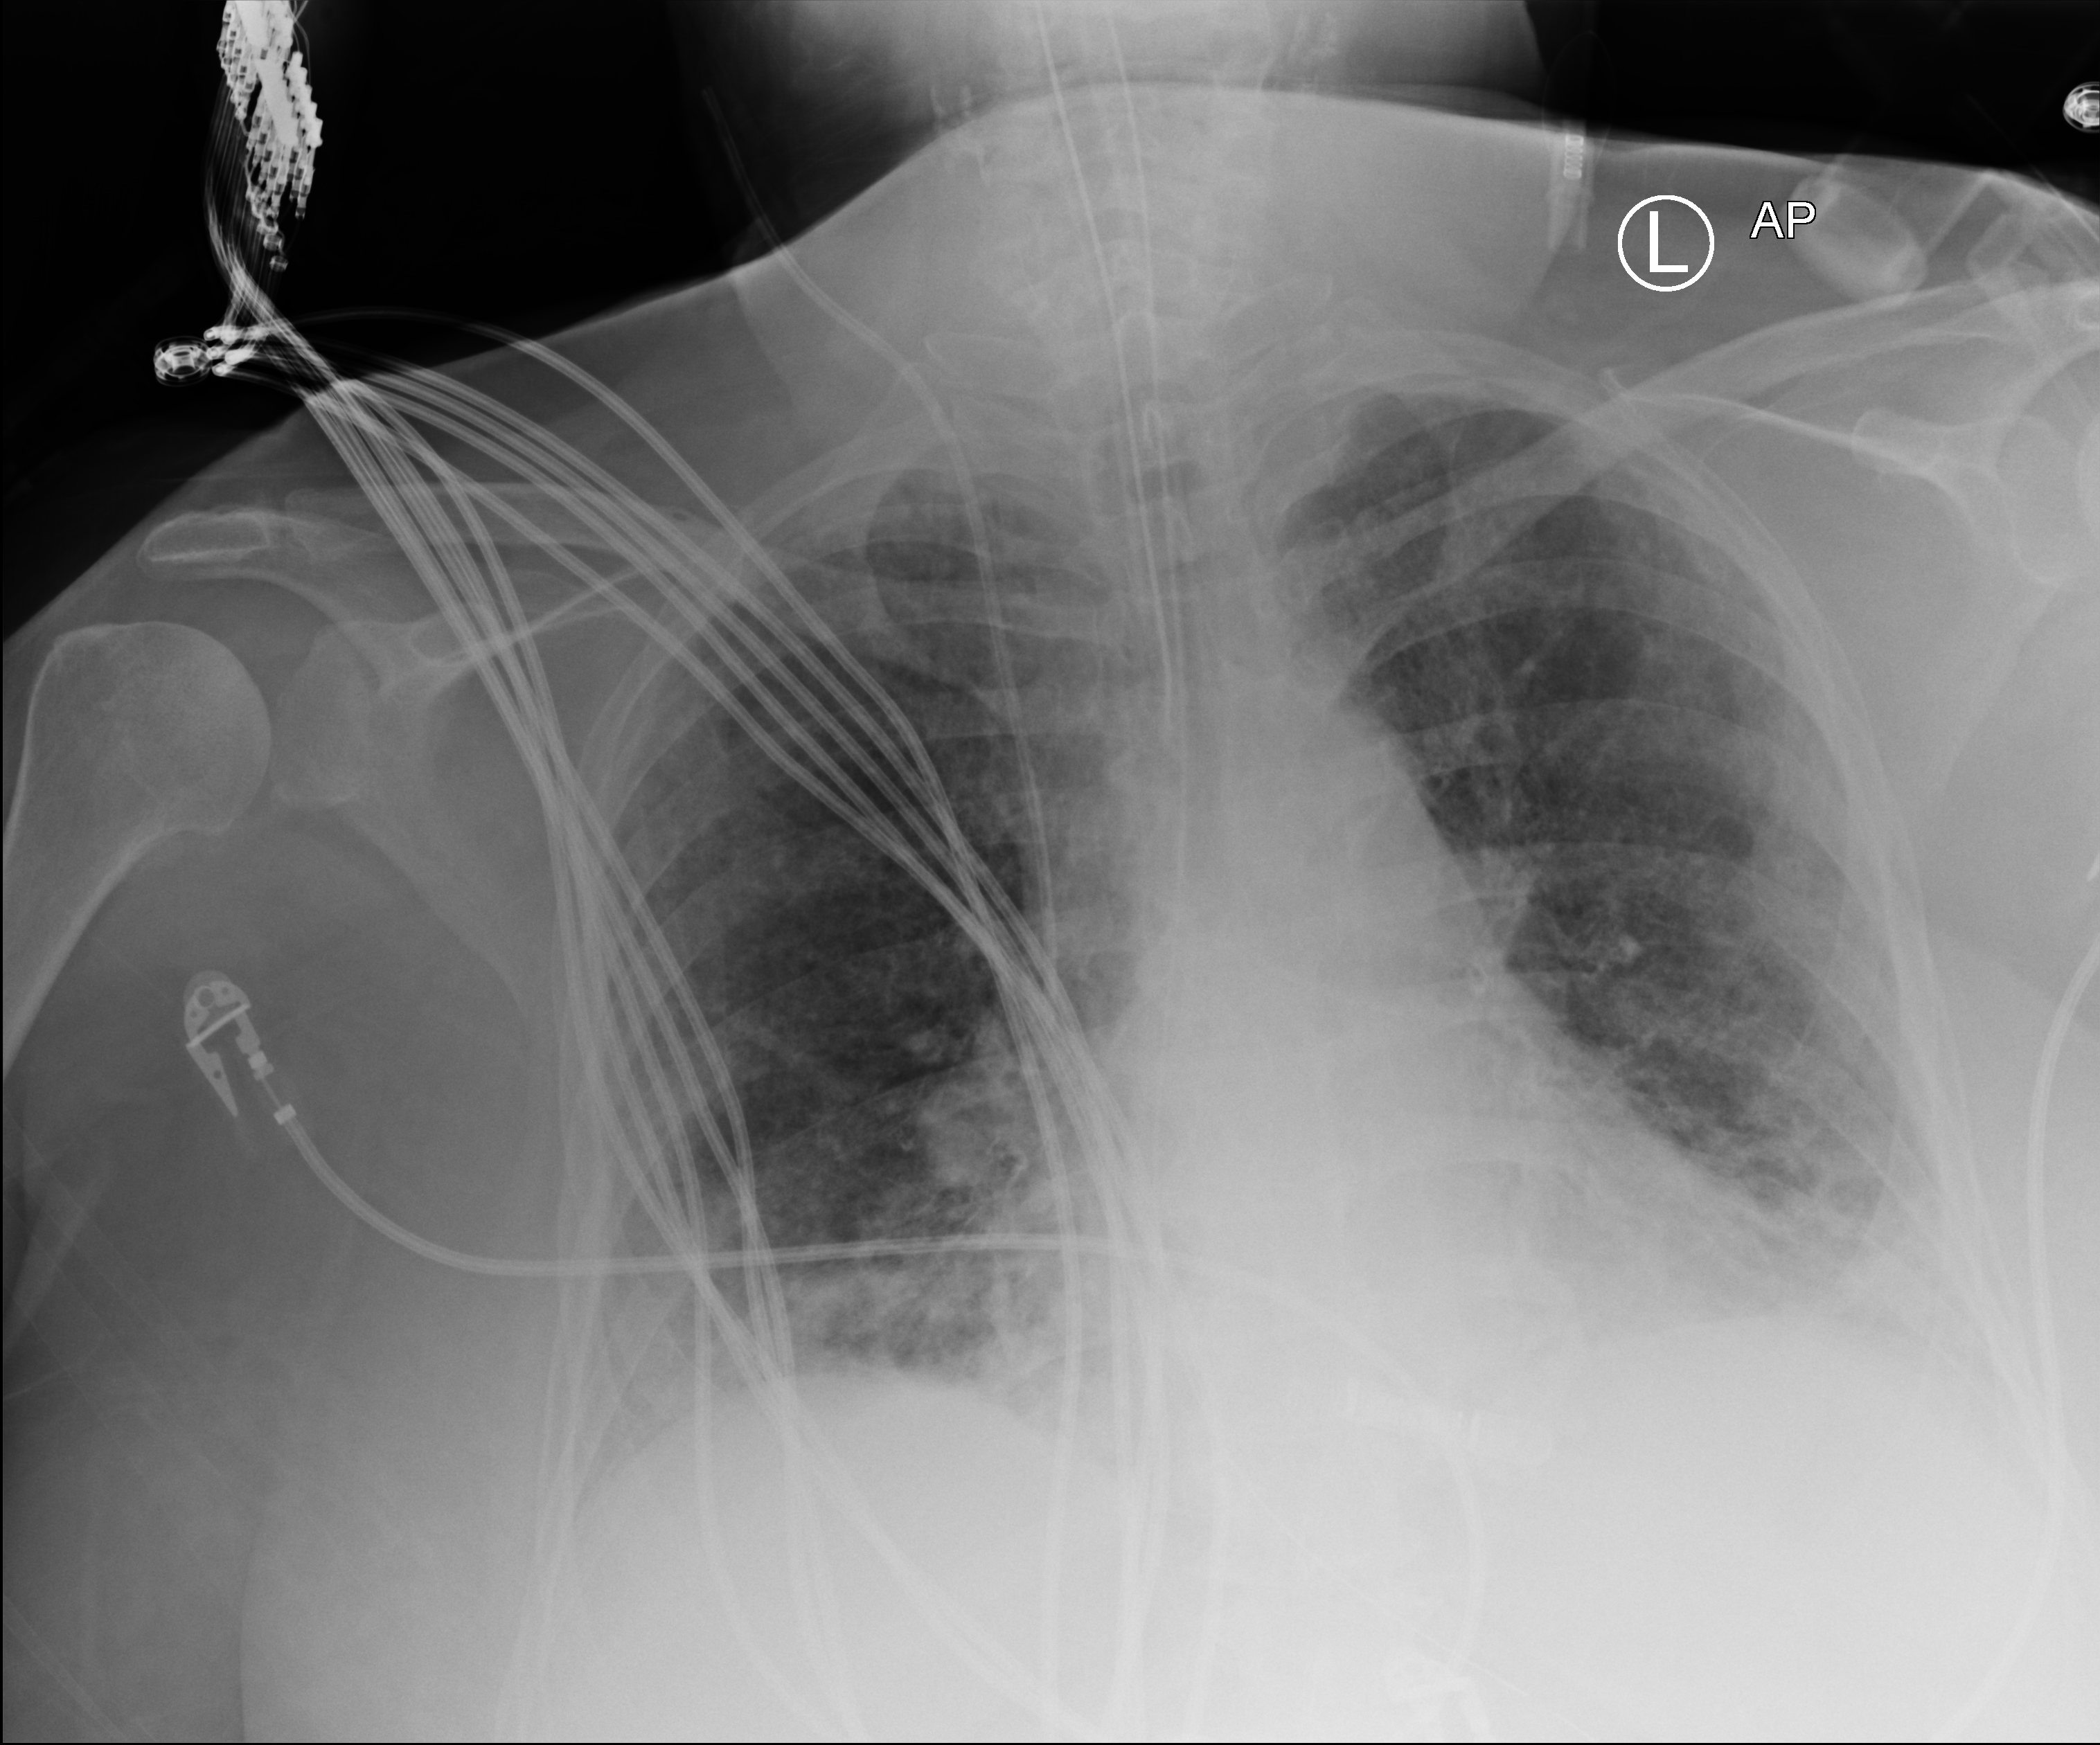
Bedside chest radiograph (computed radiography). Female patient hospitalised with COVID-19, age 60–74 years.
Admission-level facts for this patient (not findings on this image; timing relative to this image not recorded):
- length of hospital stay: 28 days
- admitted to intensive care during this hospital stay: yes